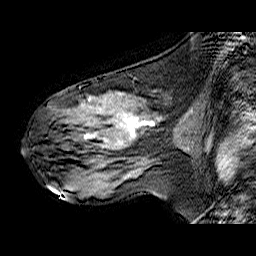
Breast MRI (dynamic contrast-enhanced), one sagittal slice; dynamic contrast-enhanced series, time point 2 of 6 at this slice position (early post-contrast); 1.5 T; TE 6.3 ms, TR 32.9 ms; 256 × 256 image matrix, field of view 200 × 200 mm. Female patient. From the clinical record (not read from this slice): setting: breast cancer imaged before/during neoadjuvant chemotherapy; receptor status: HER2-positive.
Structures marked on this image (semi-automatic segmentation, software-assisted and operator-edited):
- analysis volume of interest (the breast-tissue region the enhancement analysis was run in; not a lesion): bounding box <47,88,167,173> (left, top, right, bottom; pixels)
- tumour enhancement mask (voxels above the 100 % enhancement threshold inside the analysis volume of interest): <84,117,154,143>